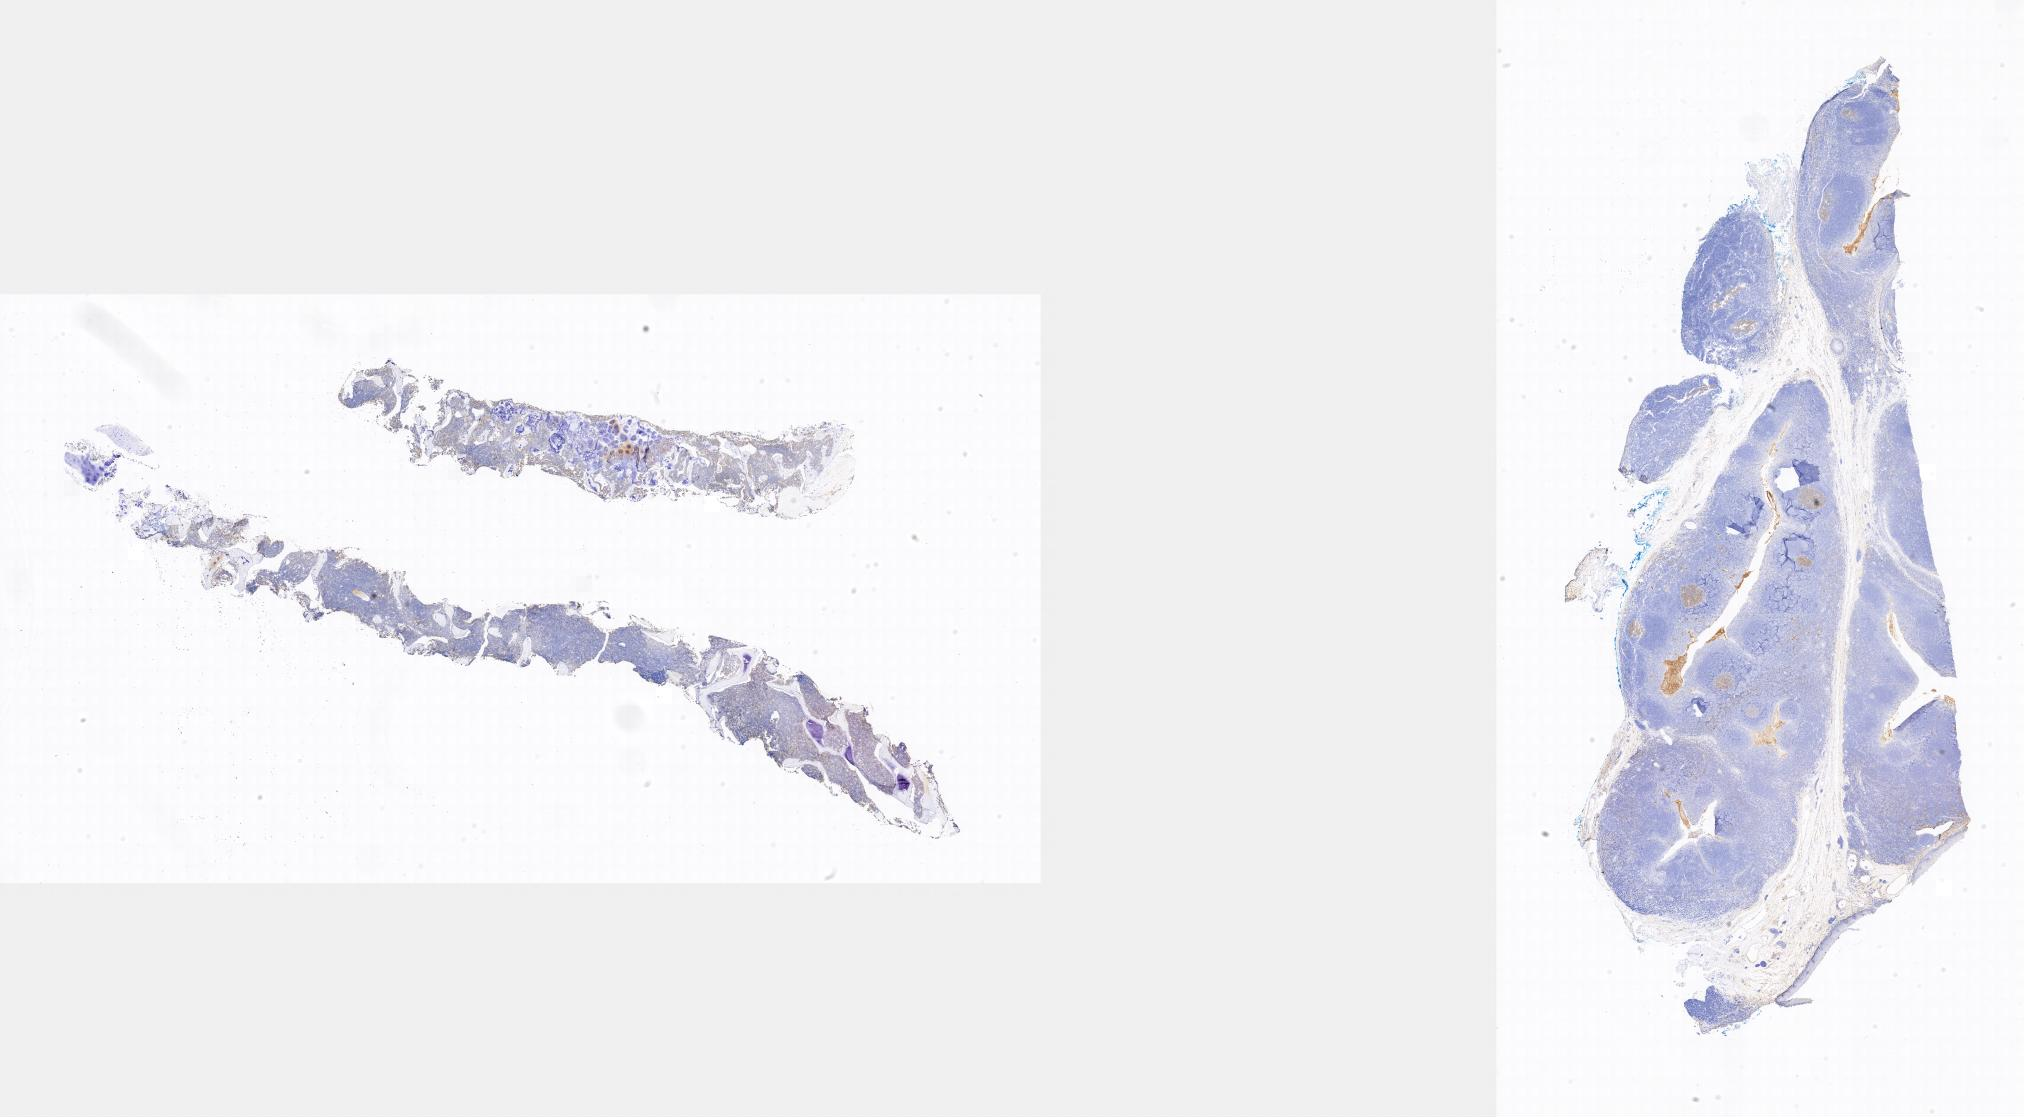
Immunohistochemistry (IHC) whole-slide image stained for CD10, a low-resolution overview of the entire scanned area; specimen: tumor tissue; anatomic site: bone marrow. Patient: male, 11 years old.
Histologic diagnosis: Burkitt lymphoma, NOS.